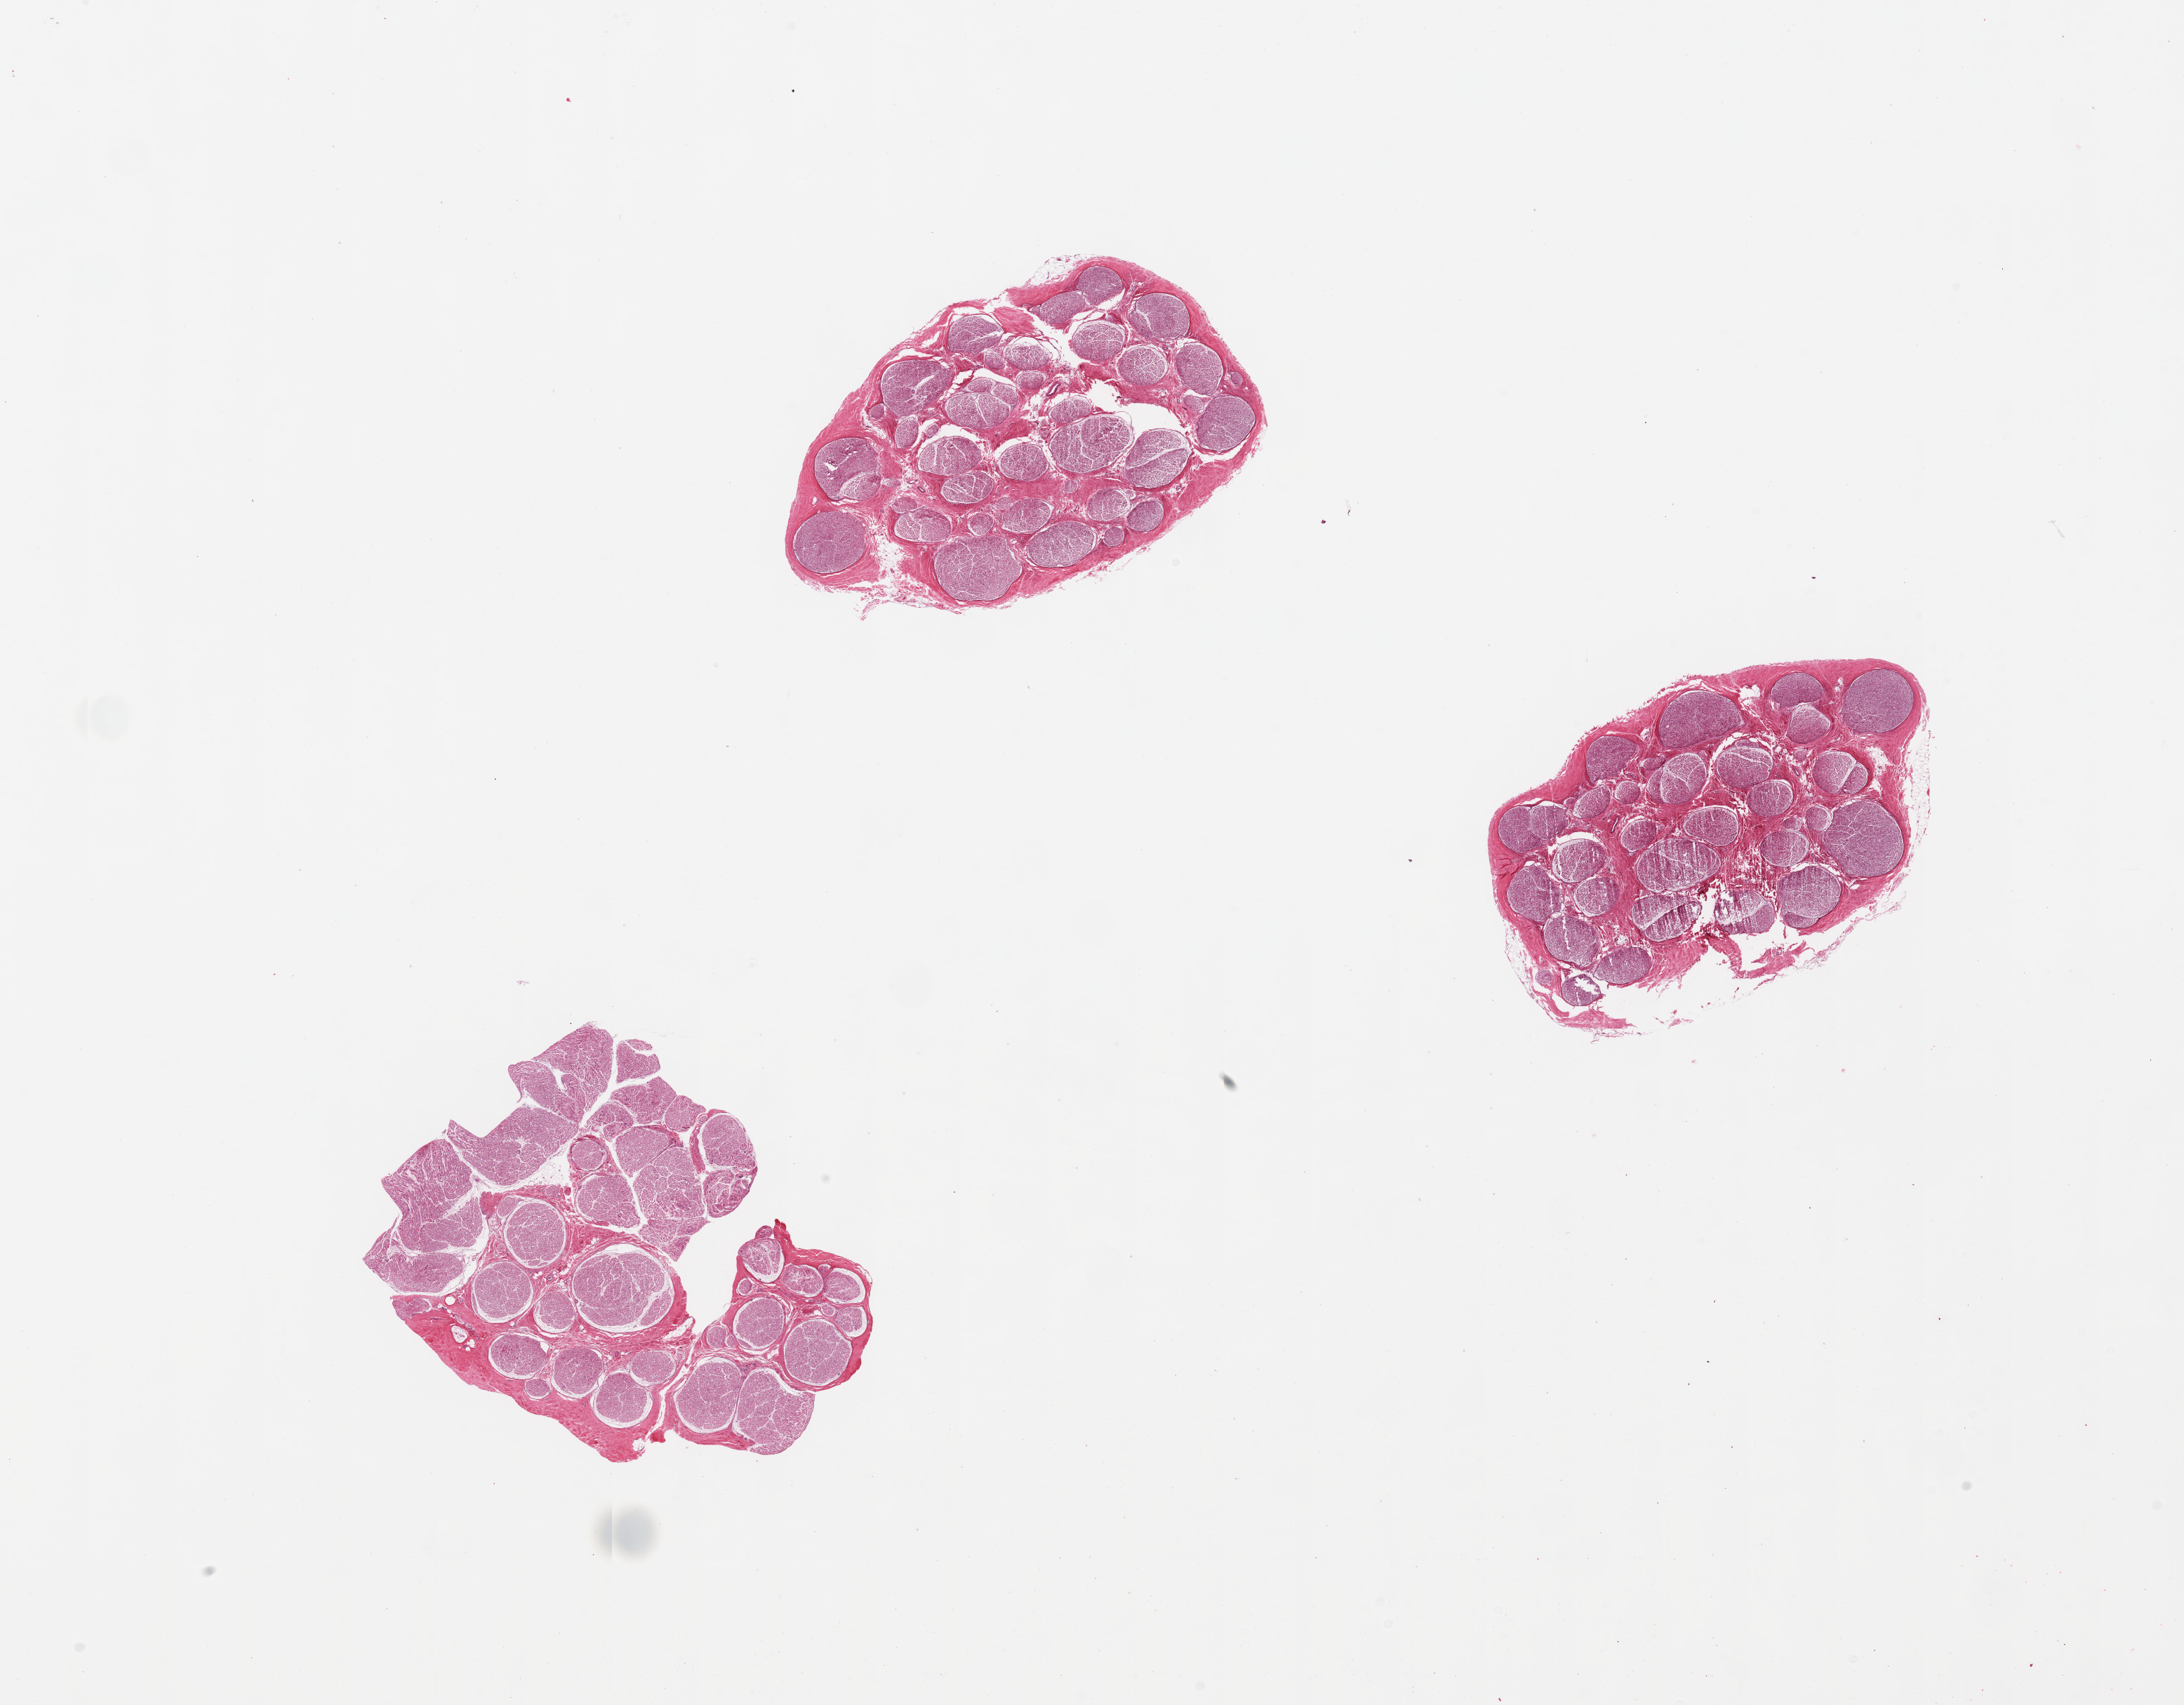
Haematoxylin and eosin whole-slide image, brightfield, shown as a low-resolution overview of the whole scanned area (about 24.6 x 19.2 mm, slide scanned at 20x), PAXgene-fixed paraffin-embedded (PFPE) section, section of tibial nerve (target tissue), tissue donor sample.
- reviewer comment on this tissue sample: 3 pieces; well trimmed